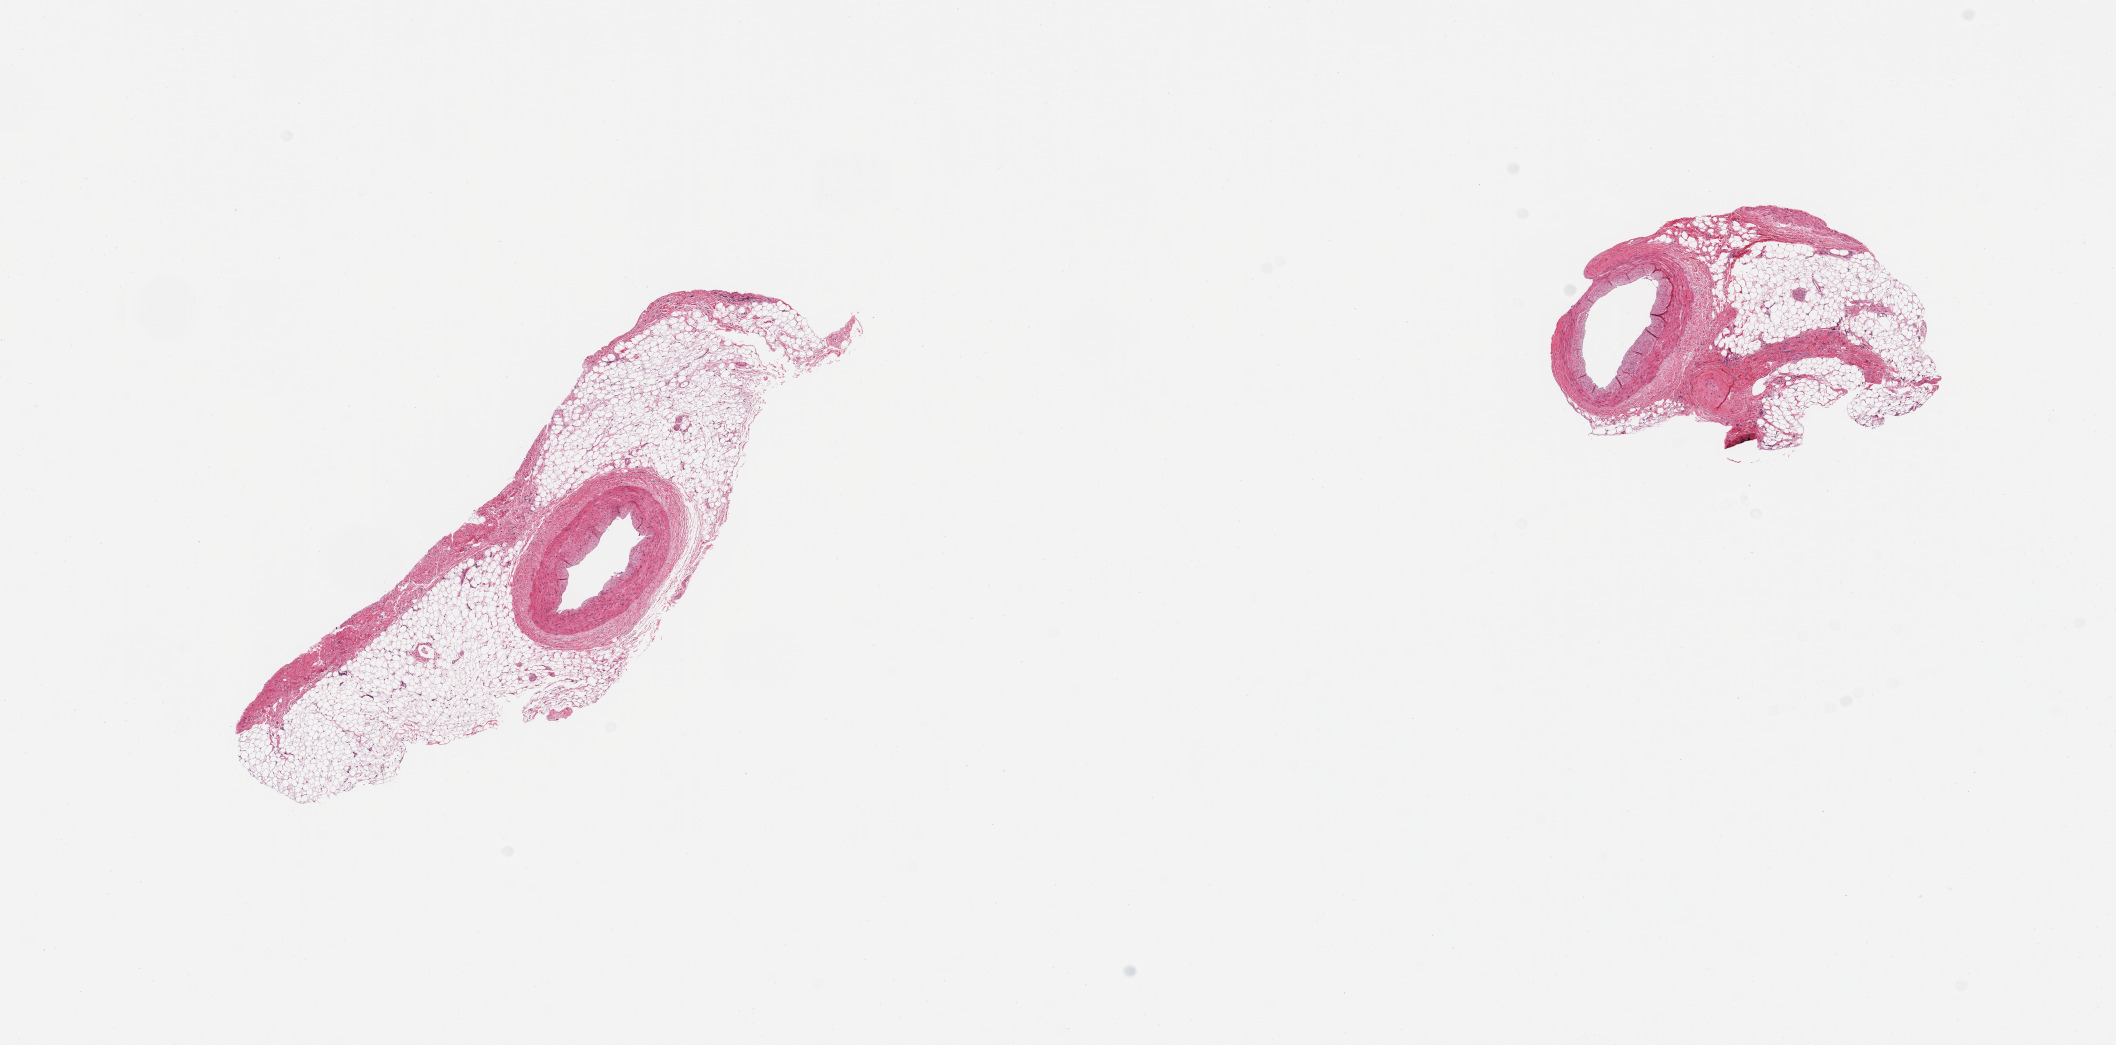
Whole-slide image, haematoxylin and eosin stain, whole scanned area (about 16.7 x 8.3 mm, from a 20x scan) shown as a low-resolution overview; PAXgene-fixed, paraffin-embedded tissue; section of coronary artery (target tissue); donor tissue sample. Male donor.
Review note (as recorded): Excessive contaminating adherent fat.